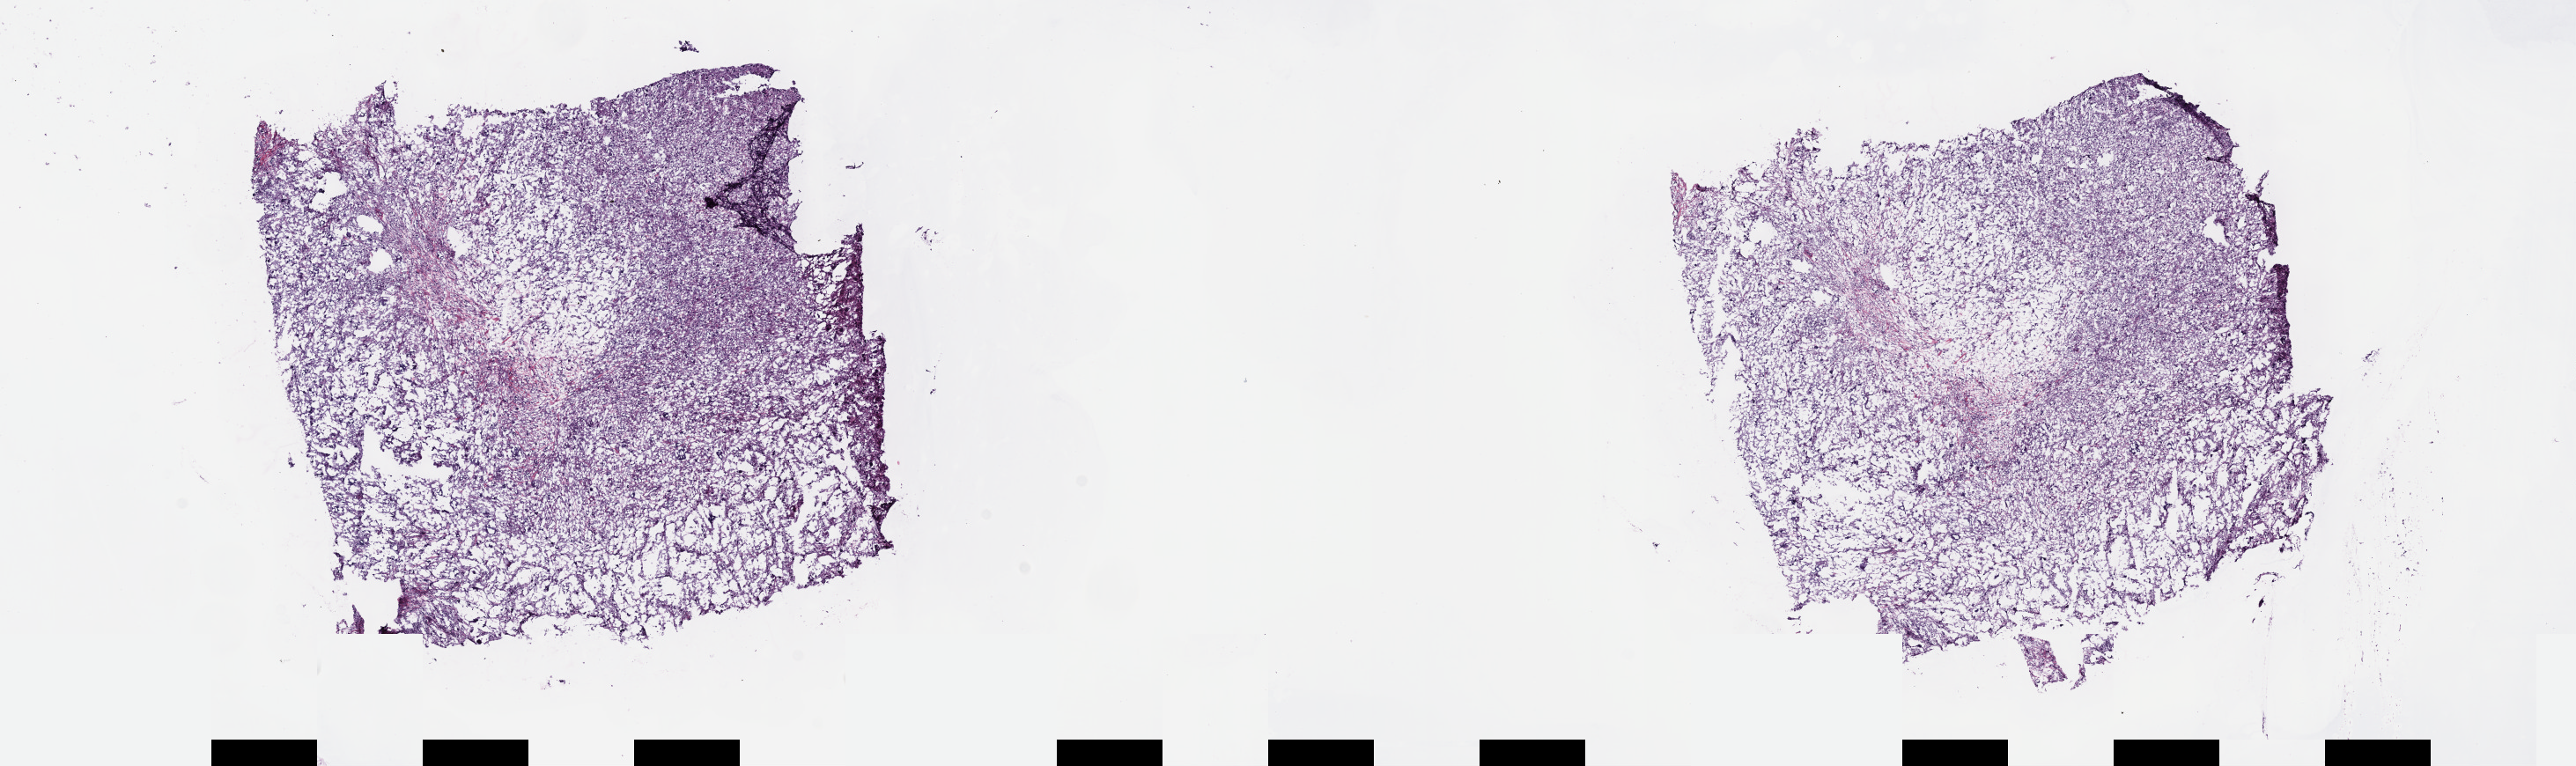
Hematoxylin and eosin (H&E) stained whole-slide image, low-resolution overview of the scanned area, about 23.7 x 7.0 mm (slide scanned at 40x); frozen section; connective, subcutaneous and other soft tissues, primary tumour sample. Female patient; age at initial diagnosis 67 years. Pathologist review of this section (percent, as recorded): tumour cells 100%, tumour nuclei 80%, normal cells 0%, stromal cells 0%, necrosis 0%. Infiltration values recorded for this section: lymphocyte infiltration 1%, monocyte infiltration 0%, neutrophil infiltration 0%.
• histologic diagnosis: Undifferentiated sarcoma